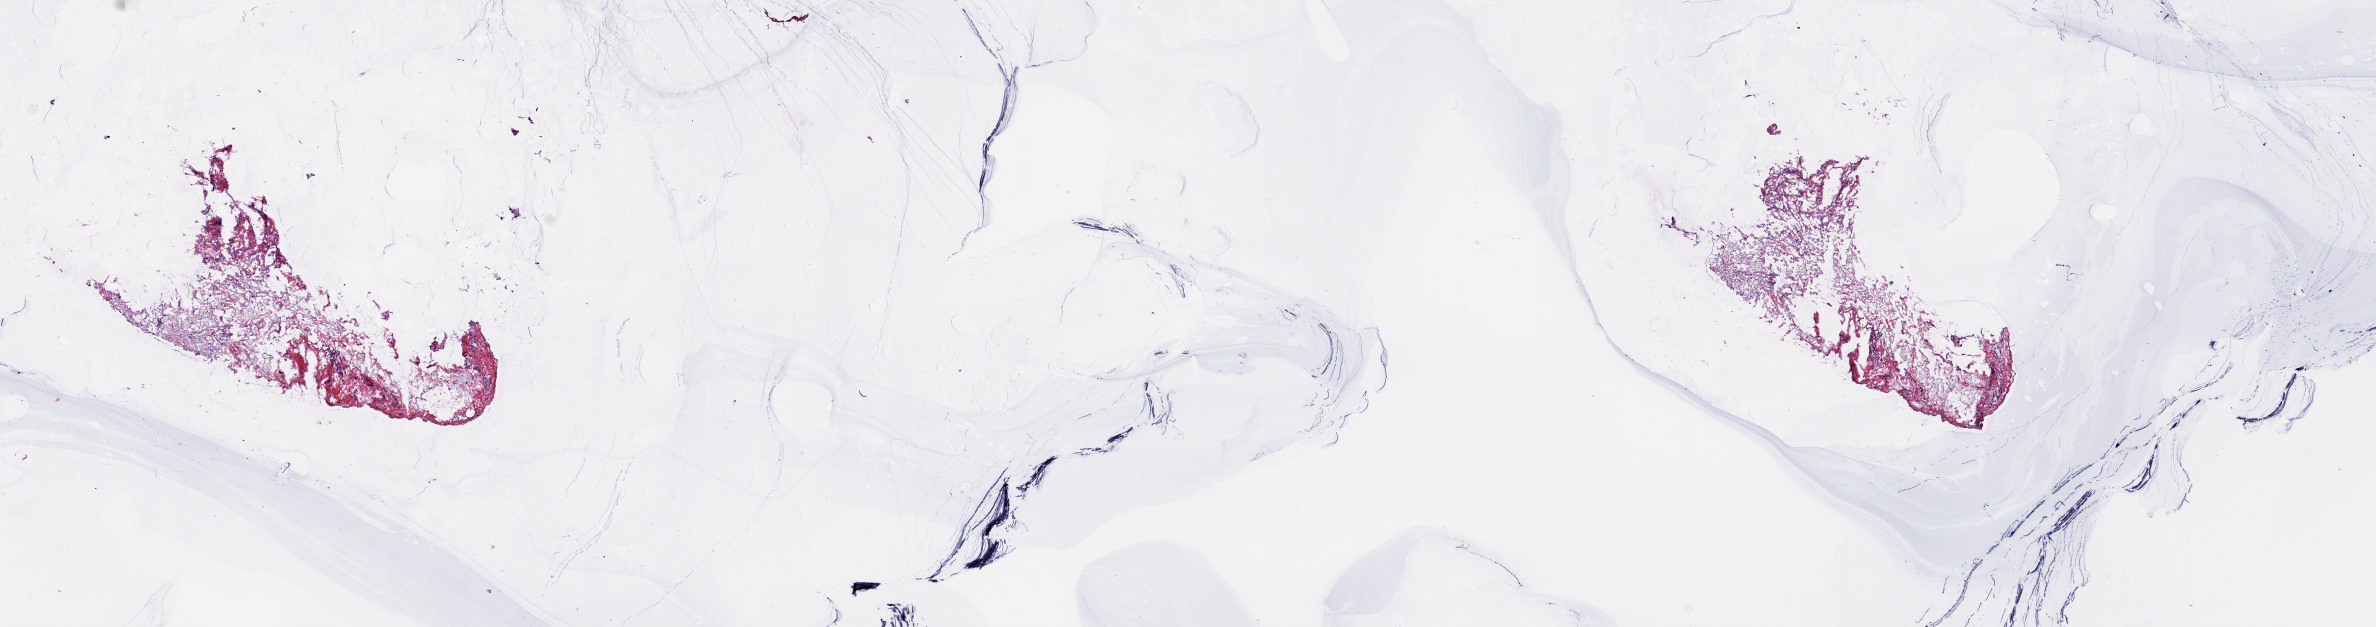
Digitized H&E tissue section (whole slide), whole scanned area (about 18.8 x 5.0 mm) shown as a low-resolution overview; frozen section from the top of the tissue portion; sample: solid tissue normal (non-tumour tissue), thymus. Male patient; age at initial diagnosis 51 years. Slide review estimates, as recorded: tumour cells 0%, tumour nuclei 0%, normal cells 100%, stromal cells 0%, necrosis 0%. Infiltration values recorded for this section: lymphocyte infiltration 1%, monocyte infiltration 0%, neutrophil infiltration 0%.
This section: solid tissue normal (non-tumour) sample from the same patient. Patient diagnosis: Thymoma, type B2, malignant.